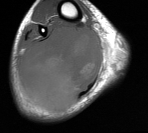
MRI of an extremity soft-tissue mass, one axial slice; slice 36 of 76 in the series (ordered by position); MR volume resampled by the dataset authors to the PET/CT grid (not the native acquisition matrix); 3.27 mm slice thickness; 148 × 133 image matrix, field of view 145 × 130 mm. Male patient. From the clinical record (not read from this slice): histological type: liposarcoma - round cell; grade: high; site of the primary tumour: right calf.
Structures marked on this image (expert contour drawn on MRI and transferred to this co-registered scan by the dataset authors):
- gross tumour volume (mass): bounding box <19,26,103,113> (left, top, right, bottom; pixels)